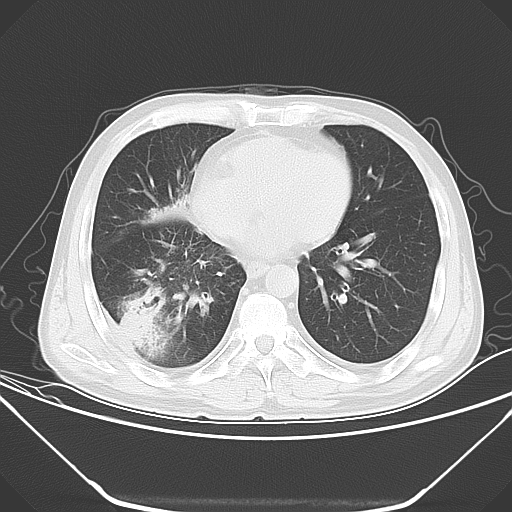
Chest CT, one axial slice. Position 18 of 52 along the scan axis. Lung window (W 1500 / L -600 HU). 5 mm slice thickness. 512 × 512 image matrix. Male patient, age 54 years. From the clinical record (not read from this slice): clinical TNM (as recorded): T2 N1 M0; histopathological grade: G3.
Structures marked on this image (bounding box drawn by a radiologist):
- lung tumour (recorded histology: adenocarcinoma): bounding box <118,286,169,361> (left, top, right, bottom; pixels)